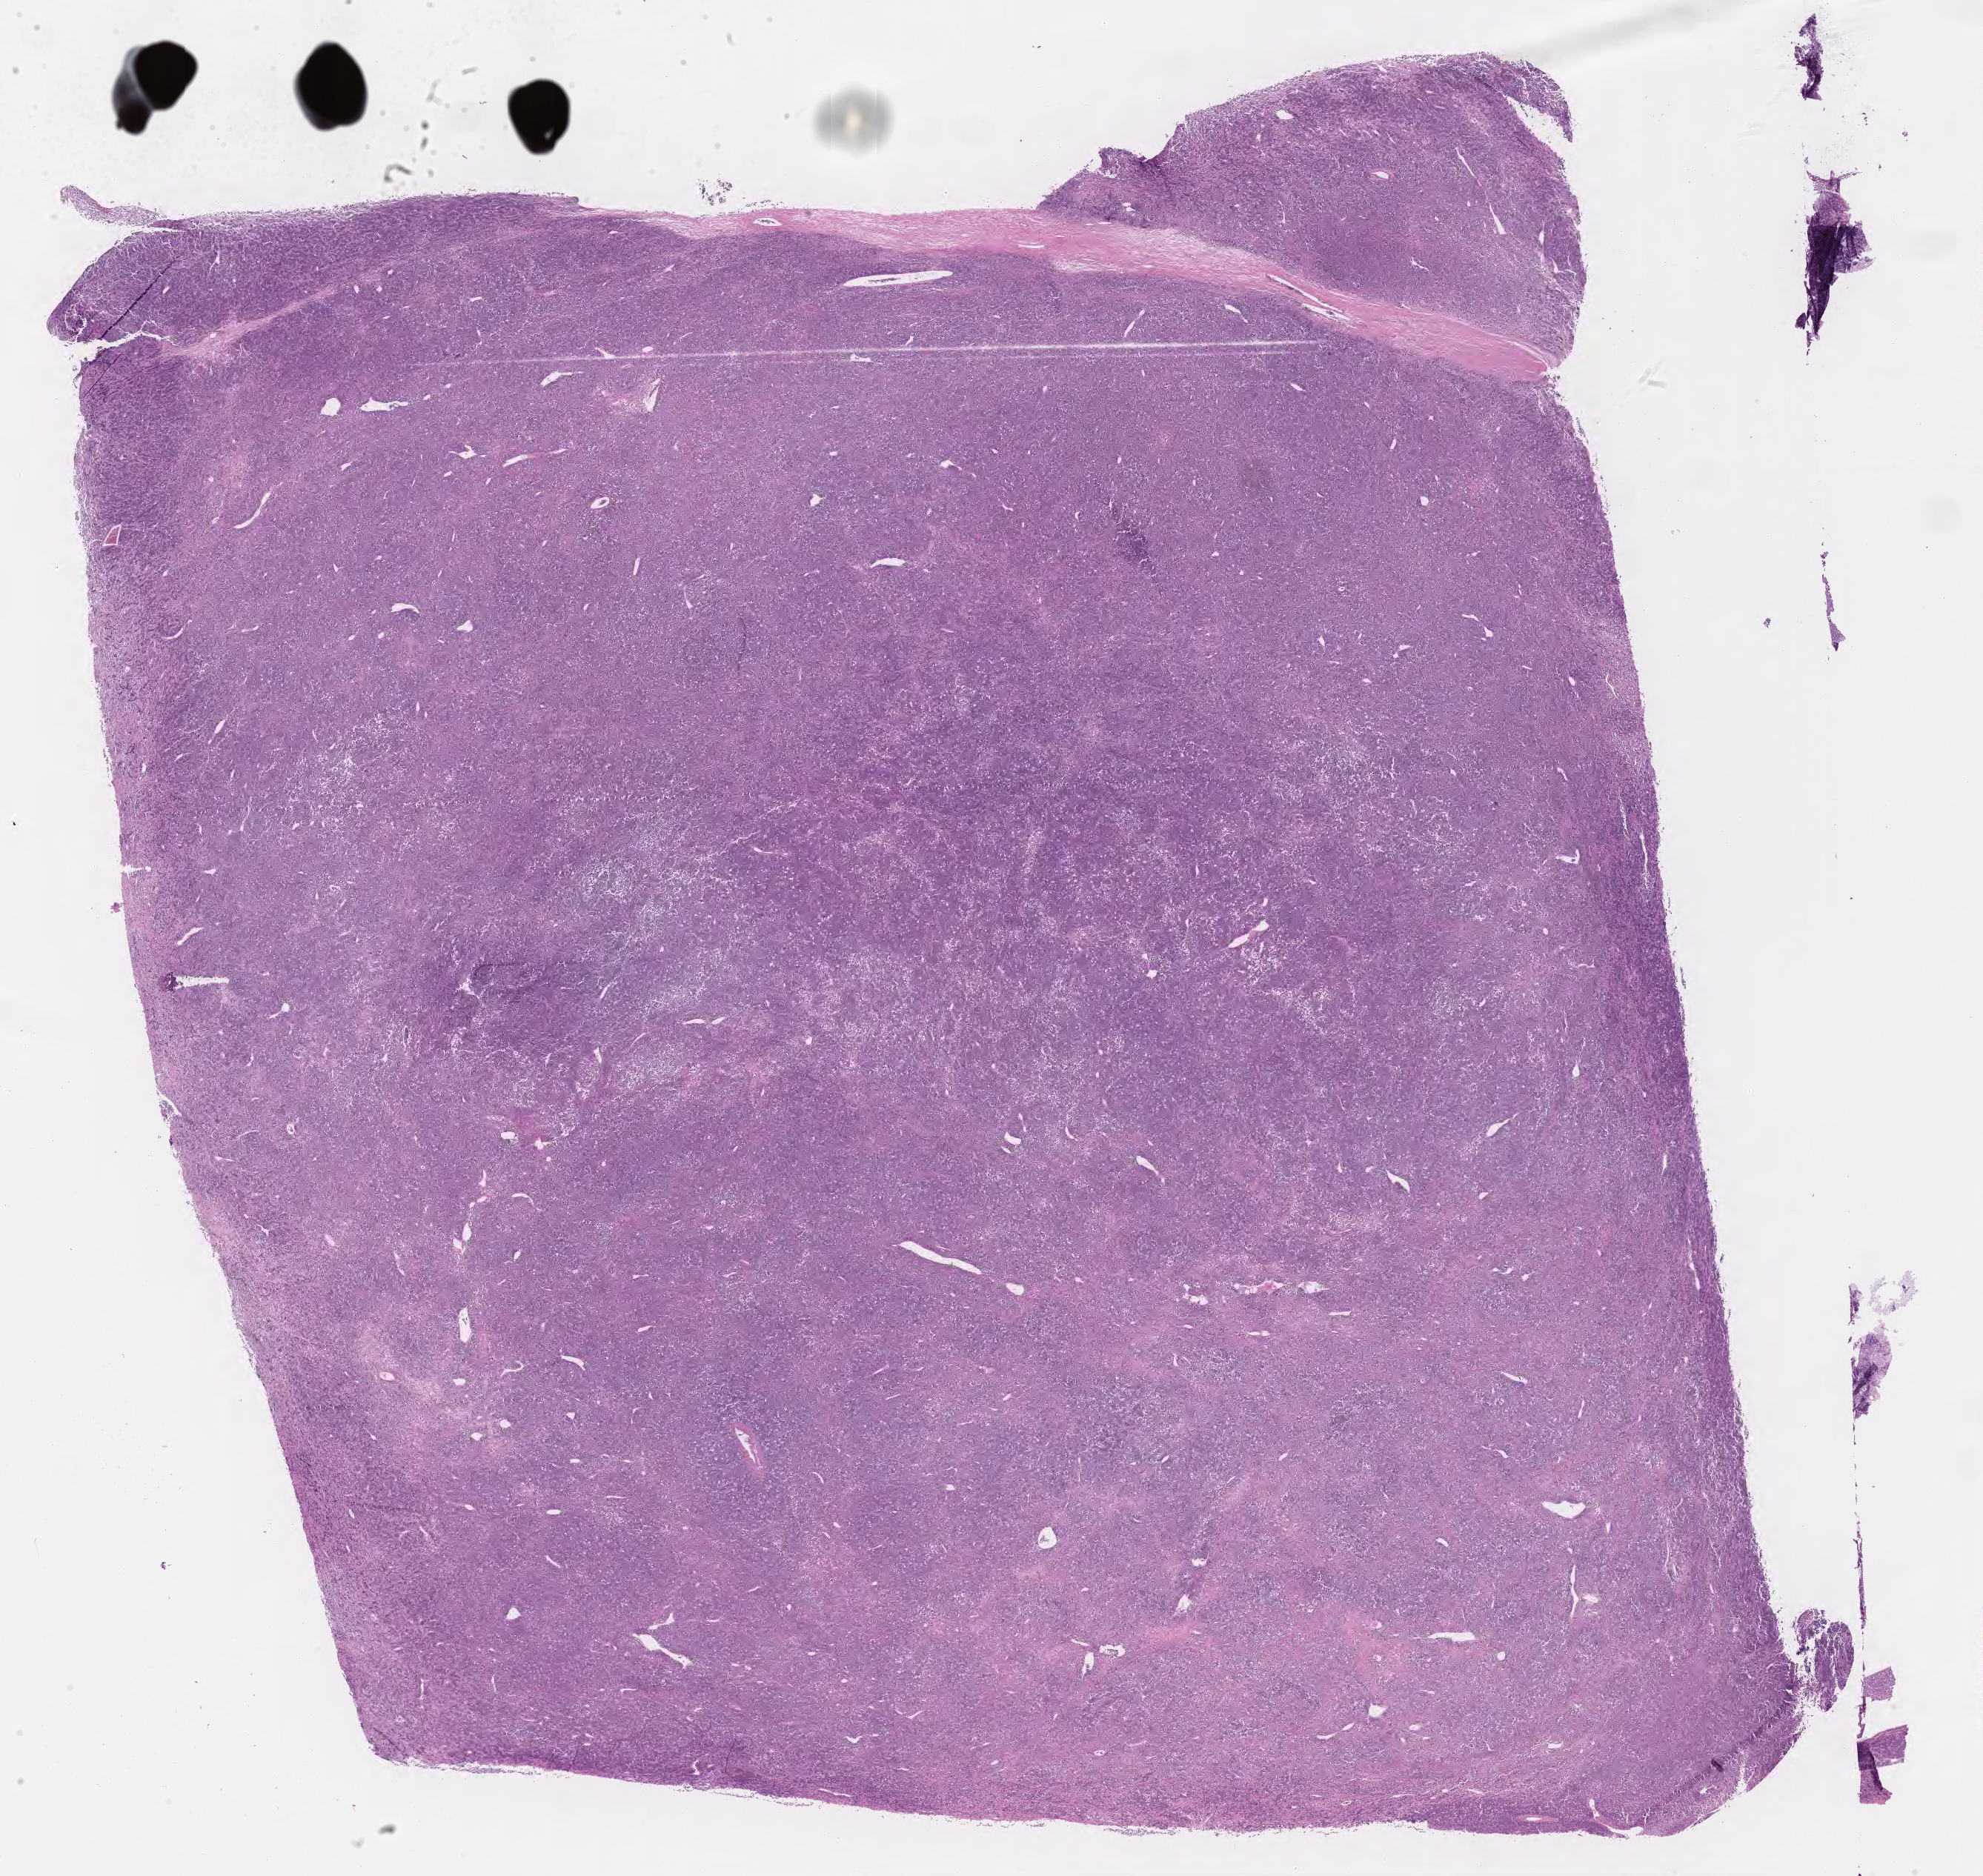
Digitized H&E-stained section, a low-resolution overview of the entire scanned area, about 21.6 x 20.5 mm, tumor tissue. Female patient, aged 22.
- histologic diagnosis: Burkitt lymphoma, NOS